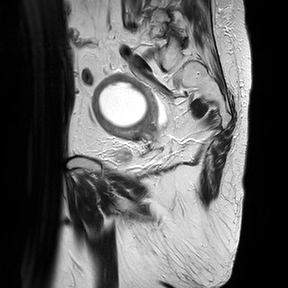
Pelvic MRI for cervical cancer, one sagittal slice; position 9 of 30 along the scan axis; T2-weighted; 1.5 T; TE 100 ms, TR 4816.3 ms; 4 mm slice thickness; 288 × 288 image matrix, field of view 300 × 300 mm. Female patient, age 74 years.
Structures marked on this image (manually delineated by an expert):
- uterus and cervix: box from (x=91, y=73) to (x=159, y=141) px